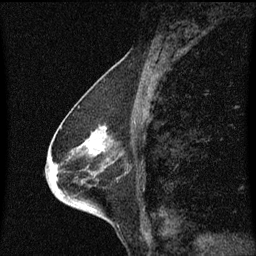
Breast MRI (dynamic contrast-enhanced), one sagittal slice; dynamic contrast-enhanced series, image 2 of 3 at this slice position (ordered by acquisition); 1.5 T; TE 4.2 ms, TR 8.4 ms; 2 mm slice thickness; 256 × 256 image matrix. Patient: female, 68 years. Case-level facts recorded for this patient, not image findings: setting: breast cancer imaged before/during neoadjuvant chemotherapy; receptor status: triple-negative.
Structures marked on this image (semi-automatic segmentation, software-assisted and operator-edited):
- analysis volume of interest (the breast-tissue region the enhancement analysis was run in; not a lesion): box from (x=41, y=114) to (x=132, y=203) px
- tumour enhancement mask (voxels above the 70 % enhancement threshold inside the analysis volume of interest): (x=55, y=128)–(x=103, y=179)